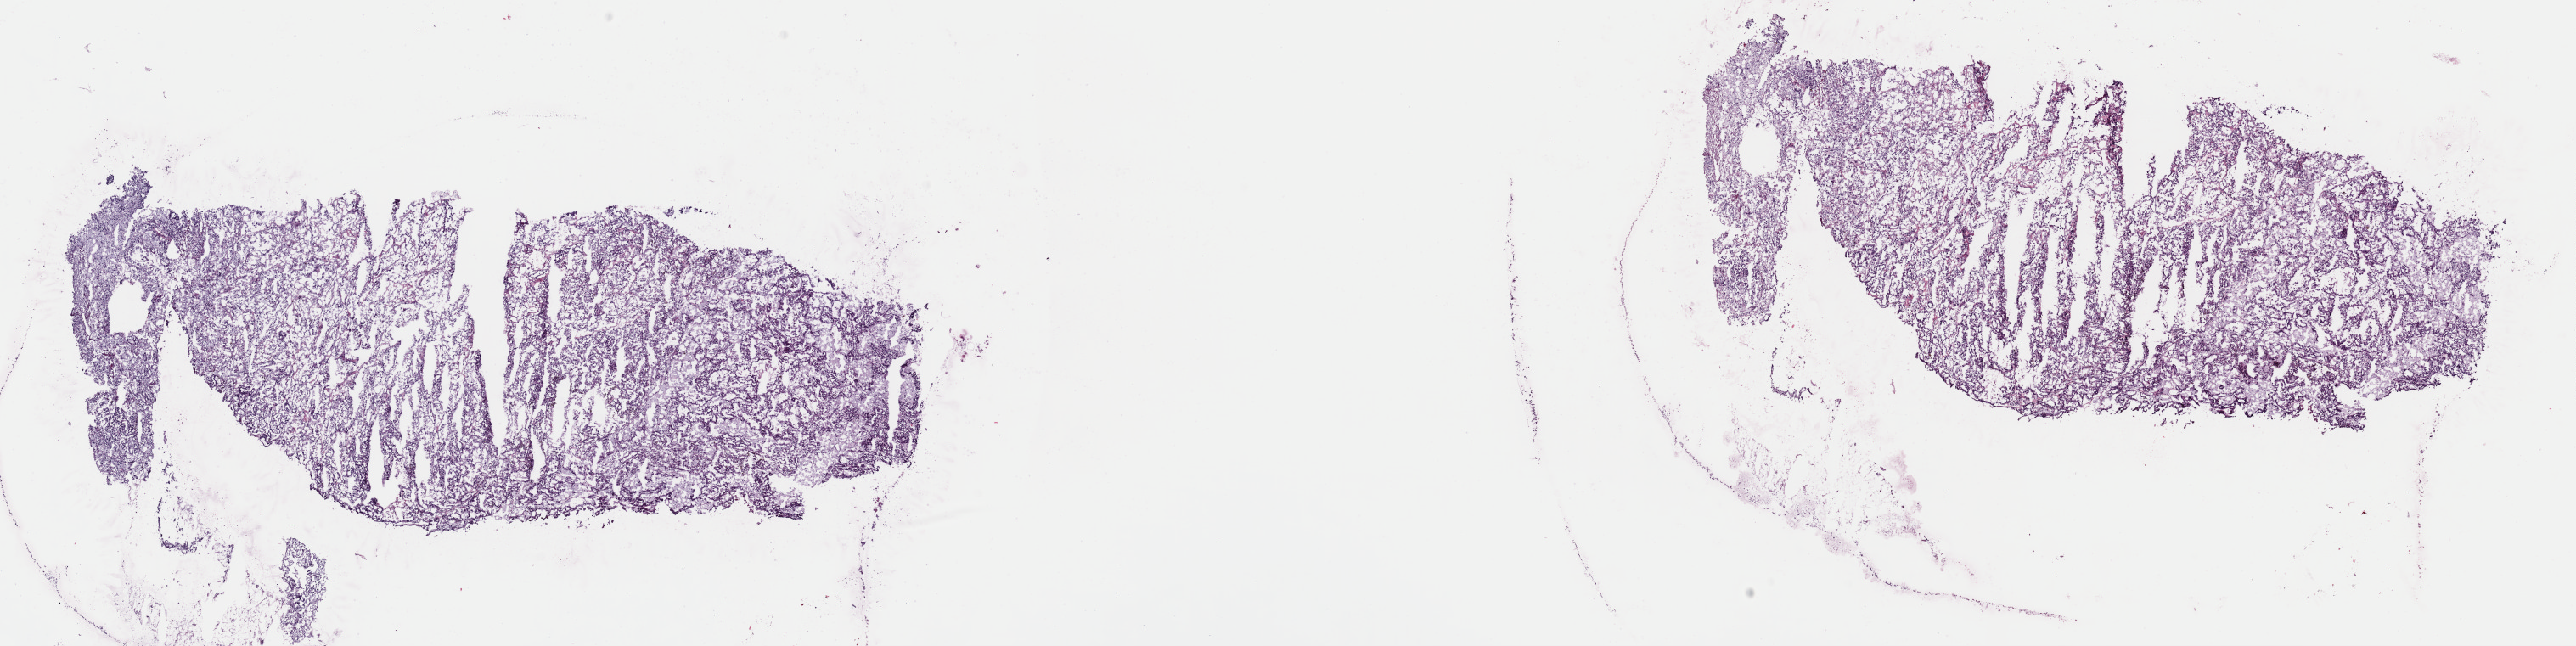
H&E whole-slide image, low-resolution overview of the scanned area, about 24.0 x 6.0 mm; frozen section from the top of the tissue portion; sample: primary tumour, kidney. Female patient; age at initial diagnosis 54 years.
Histologic diagnosis: Papillary adenocarcinoma, NOS.